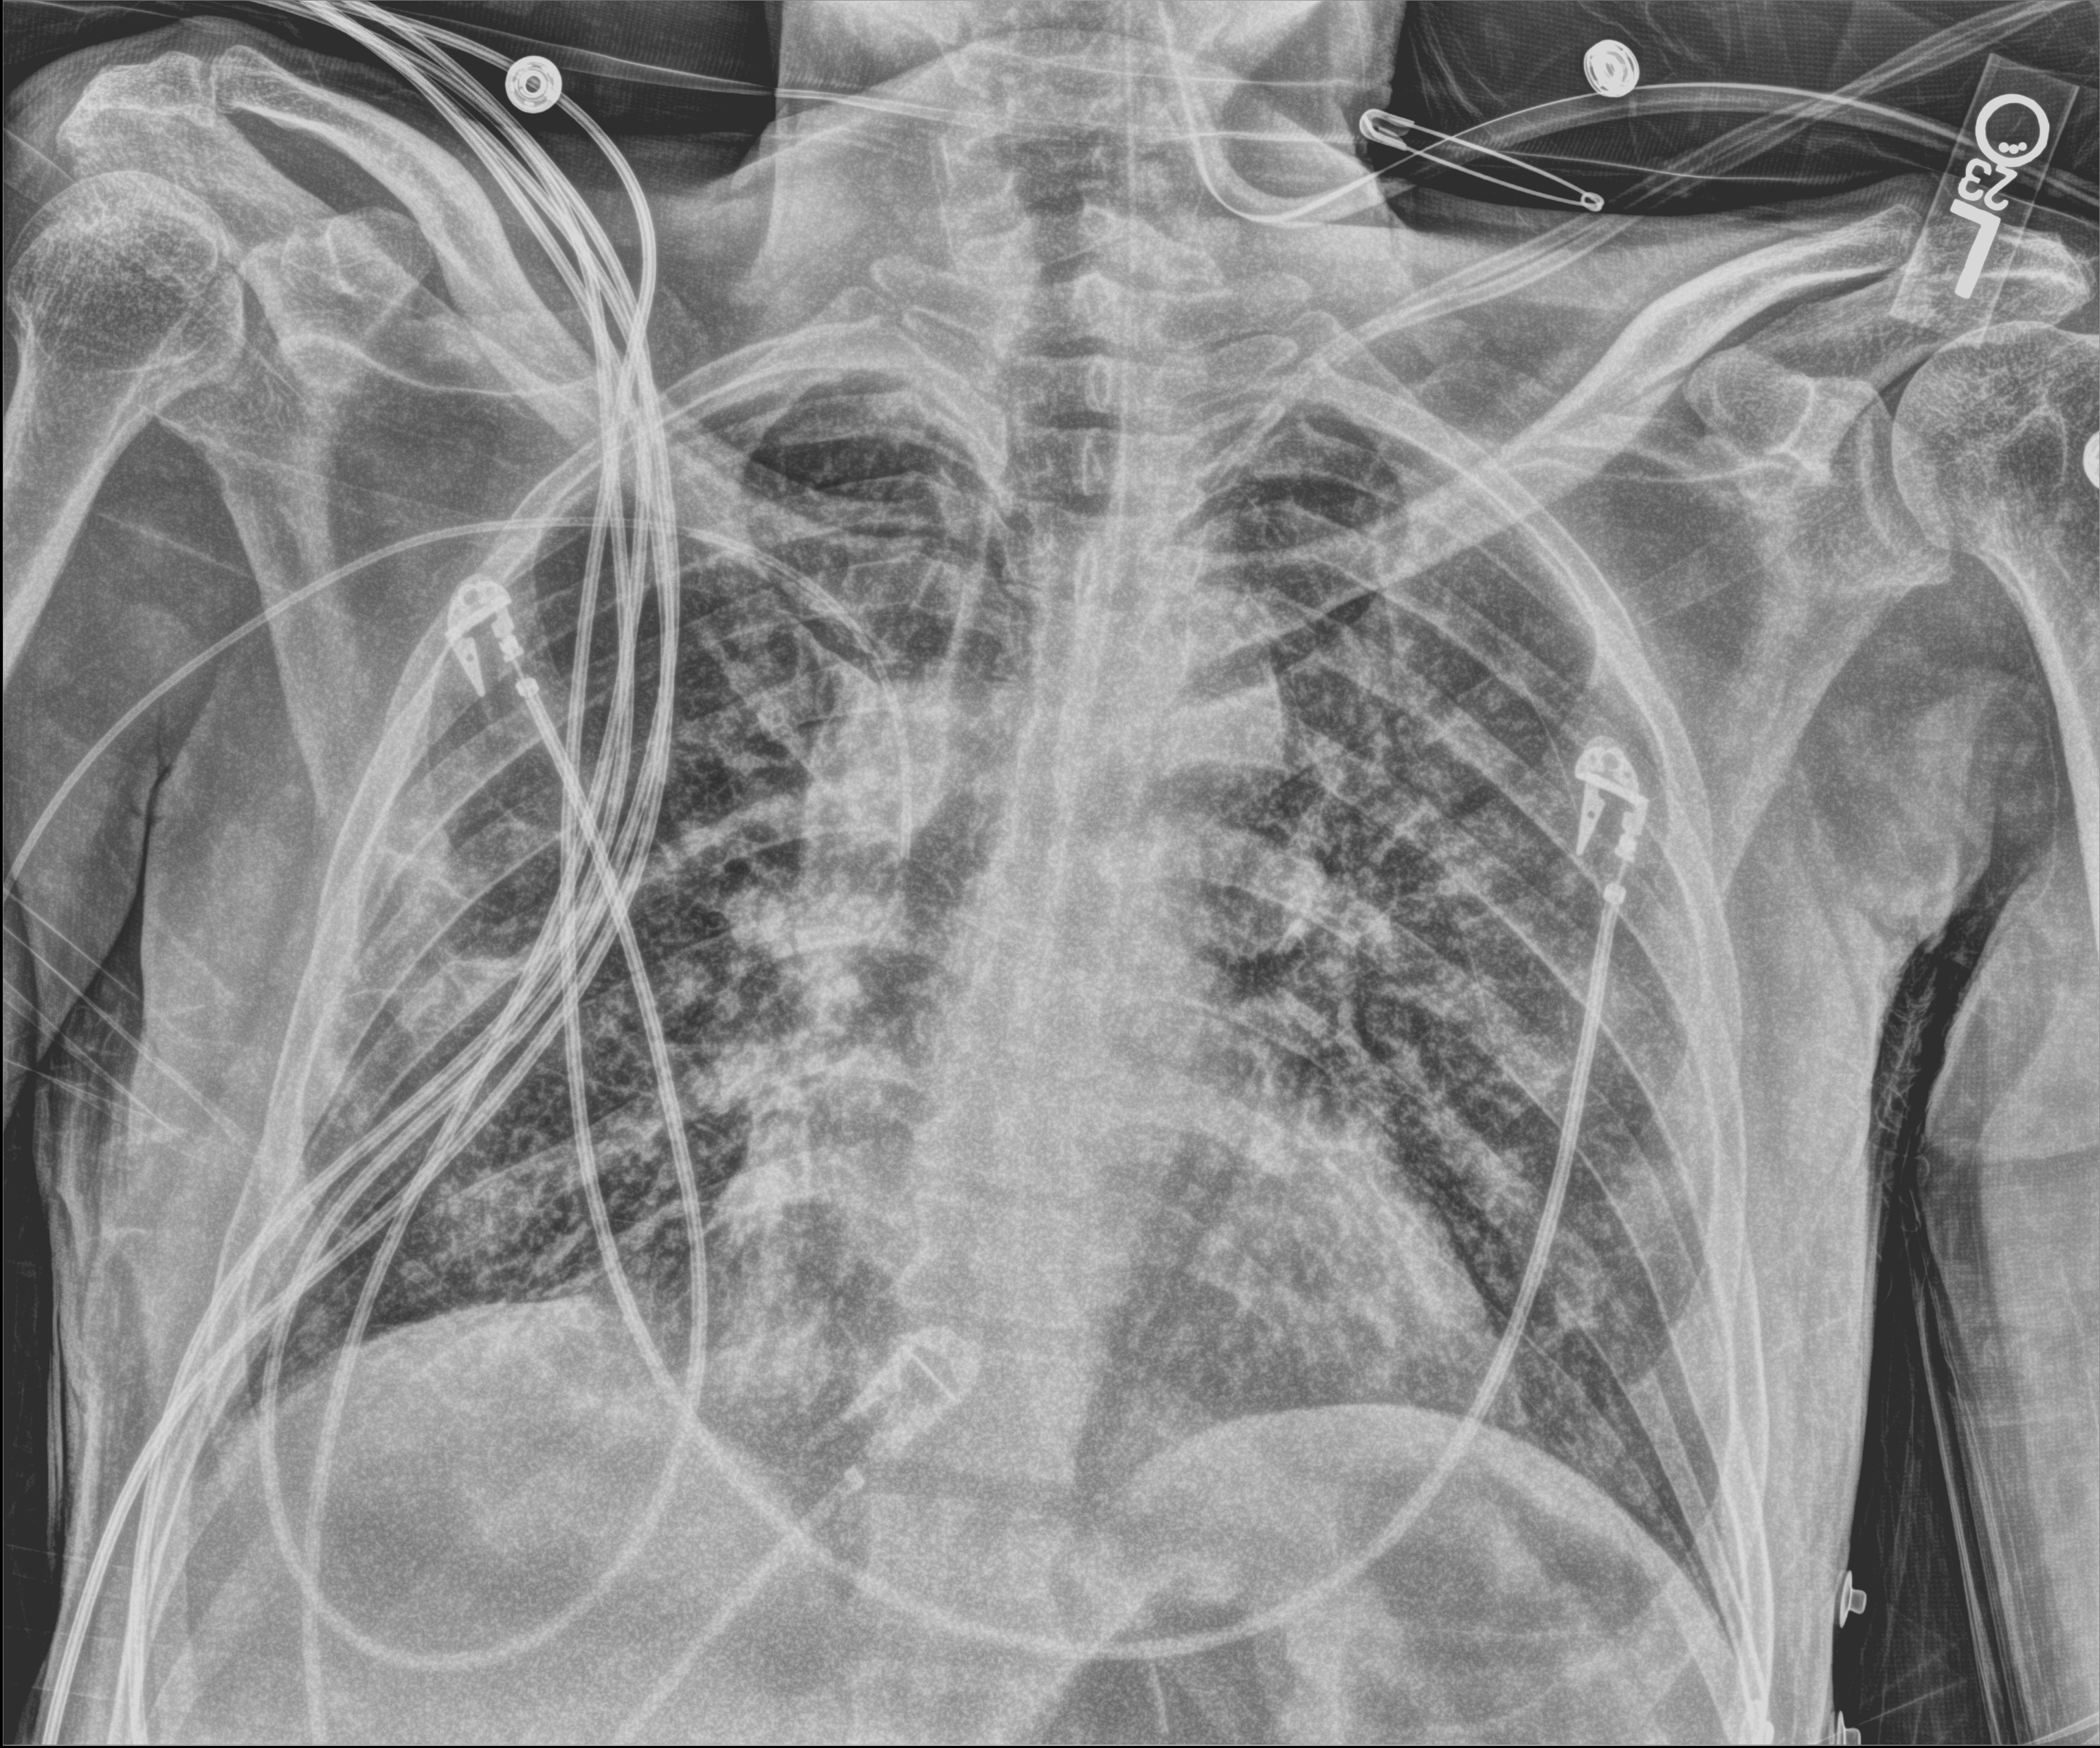
Bedside chest radiograph (computed radiography). Patient hospitalised with COVID-19; male, aged 18–59 years.
Admission-level facts for this patient (not findings on this image; timing relative to this image not recorded): admitted to intensive care during this hospital stay: yes; hypertension (admission record): no; mechanically ventilated during this hospital stay: yes.